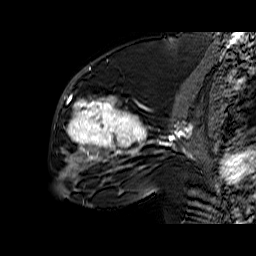
Breast MRI (dynamic contrast-enhanced), one sagittal slice; slice 30 of 60 in the series (ordered by position); dynamic contrast-enhanced series, time point 2 of 6 at this slice position (early post-contrast); 1.5 T; TE 6.4 ms, TR 32.9 ms; 256 × 256 image matrix, field of view 200 × 200 mm. Female patient. From the clinical record (not read from this slice): setting: breast cancer imaged before/during neoadjuvant chemotherapy; receptor status: triple-negative.
Annotated regions visible in this slice (semi-automatic segmentation, software-assisted and operator-edited):
- analysis volume of interest (the breast-tissue region the enhancement analysis was run in; not a lesion): box from (x=56, y=65) to (x=158, y=174) px
- tumour enhancement mask (voxels above the 100 % enhancement threshold inside the analysis volume of interest): (x=64, y=96)–(x=146, y=172)